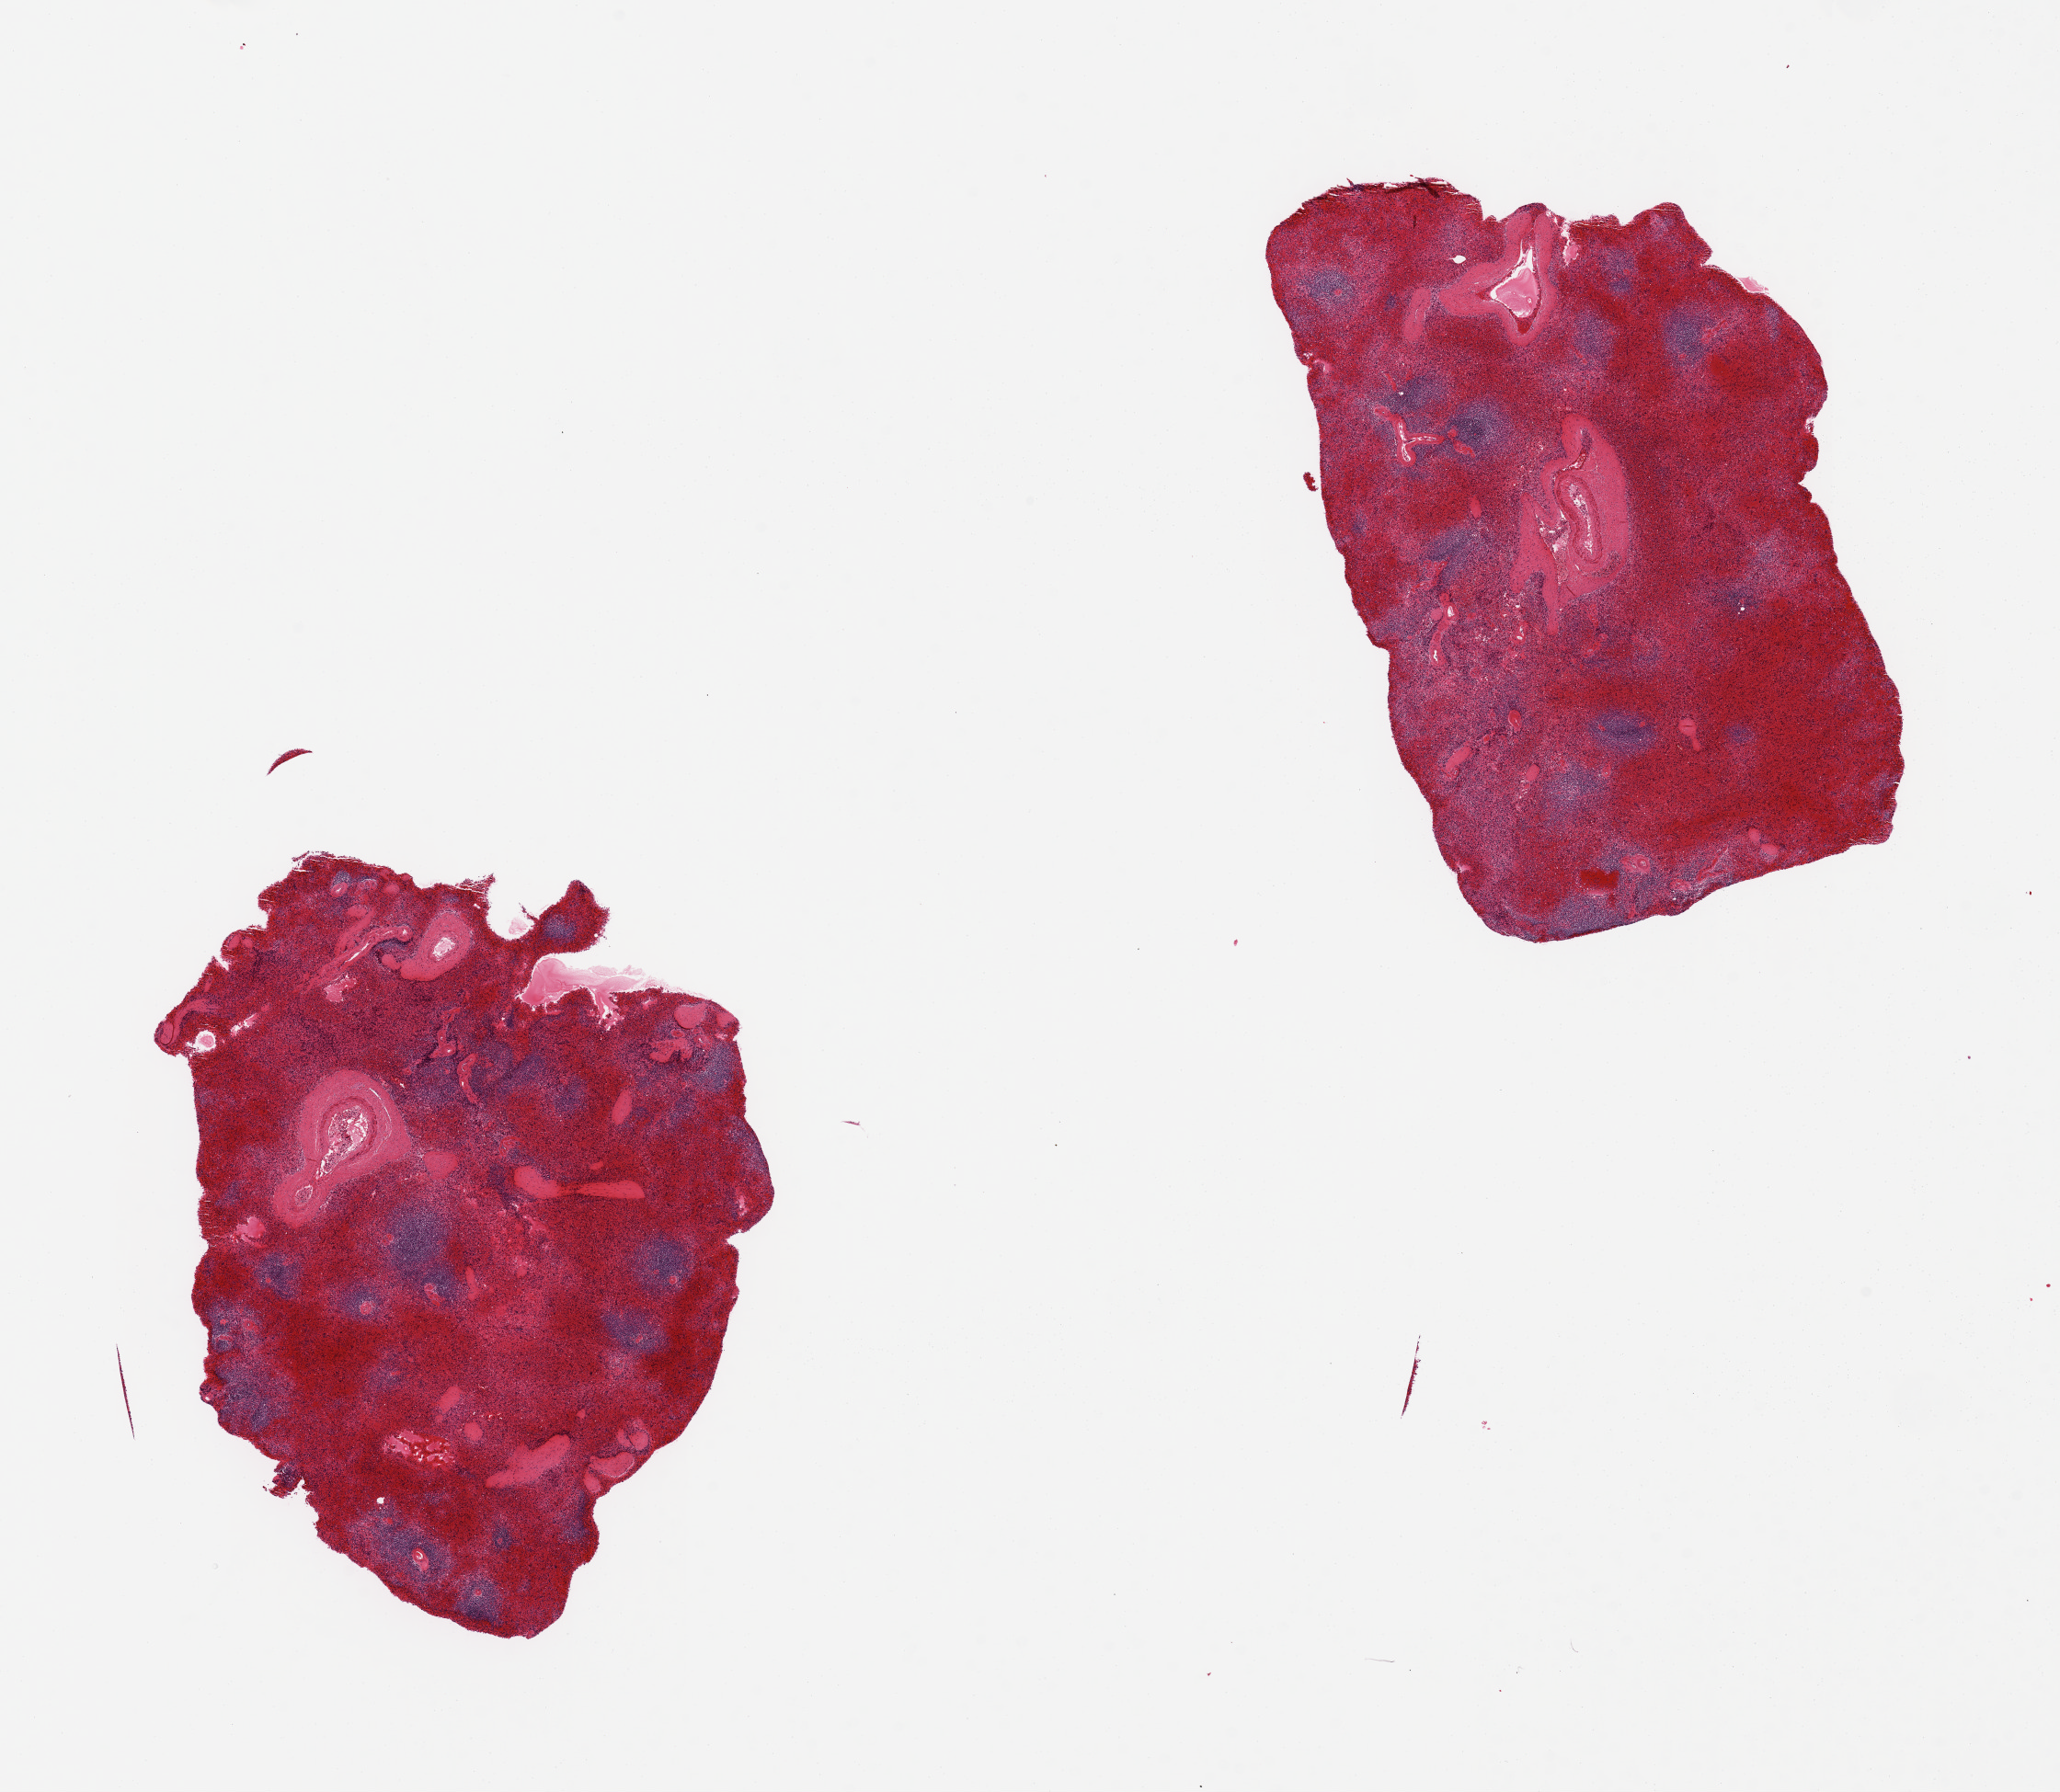
Digitized haematoxylin and eosin-stained section — low-resolution overview of the scanned area, about 17.7 x 15.4 mm (slide scanned at 20x), PAXgene-fixed paraffin-embedded (PFPE) section, target tissue: spleen, donor tissue sample. Donor: female.
• reviewer comment on this tissue sample: 2 pieces, moderate congestion